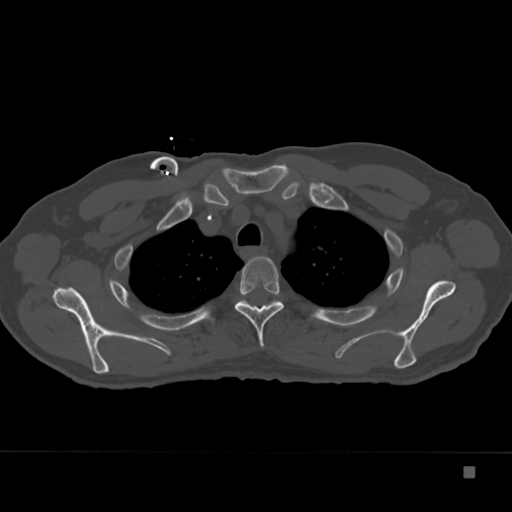
CT including the spine, one axial slice. Position 285 of 332 along the scan axis. Reconstruction kernel Br40s. 120 kVp. Bone window (W 1800 / L 400 HU). 1.5 mm slice thickness. 512 × 512 image matrix. Patient: male, 72 years. From the clinical record (not read from this slice): primary cancer: skeletal.
Outlined on this slice (semi-automatic segmentation, software-assisted and operator-edited):
- T3 vertebra: bounding box (x1, y1, x2, y2) in pixels: (234, 256, 284, 348)
- T4 vertebra: (244, 300, 278, 302)